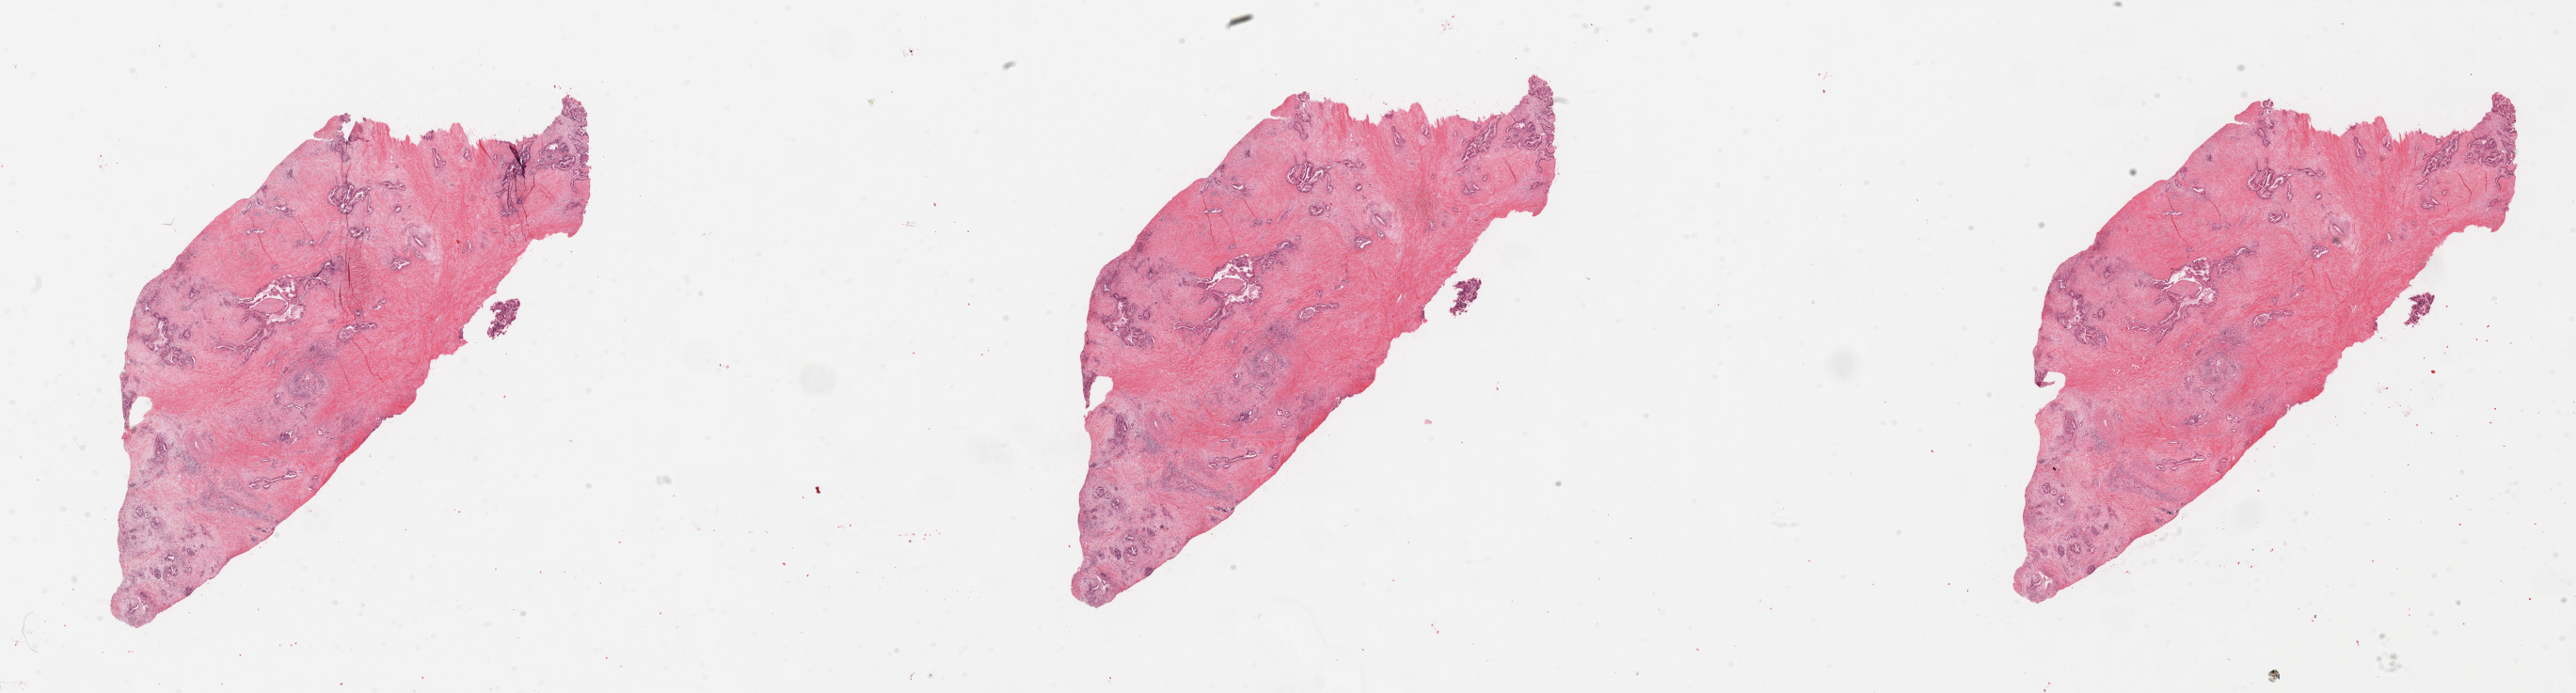
Whole-slide histology image, H&E-stained — low-resolution overview of the scanned area, about 43.3 x 11.7 mm (acquisition: 20x scan), tumour tissue sample, sampled site: pancreas. Male, 55 y/o.
Diagnosis: Infiltrating duct carcinoma, NOS.